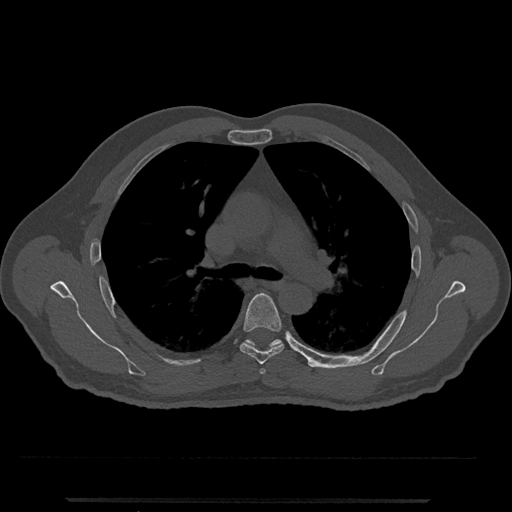
CT including the spine, one axial slice; position 782 of 797 along the scan axis; reconstruction kernel Br40s/3; bone window (W 1800 / L 400 HU); 0.5 mm slice thickness; 512 × 512 image matrix, field of view 419 × 419 mm. Male patient, age 63 years. From the clinical record (not read from this slice): primary cancer: prostate.
Annotated regions visible in this slice (semi-automatic segmentation, software-assisted and operator-edited):
- T5 vertebra: bounding box (x1, y1, x2, y2) in pixels: (239, 293, 284, 365)
- T6 vertebra: (244, 339, 282, 347)